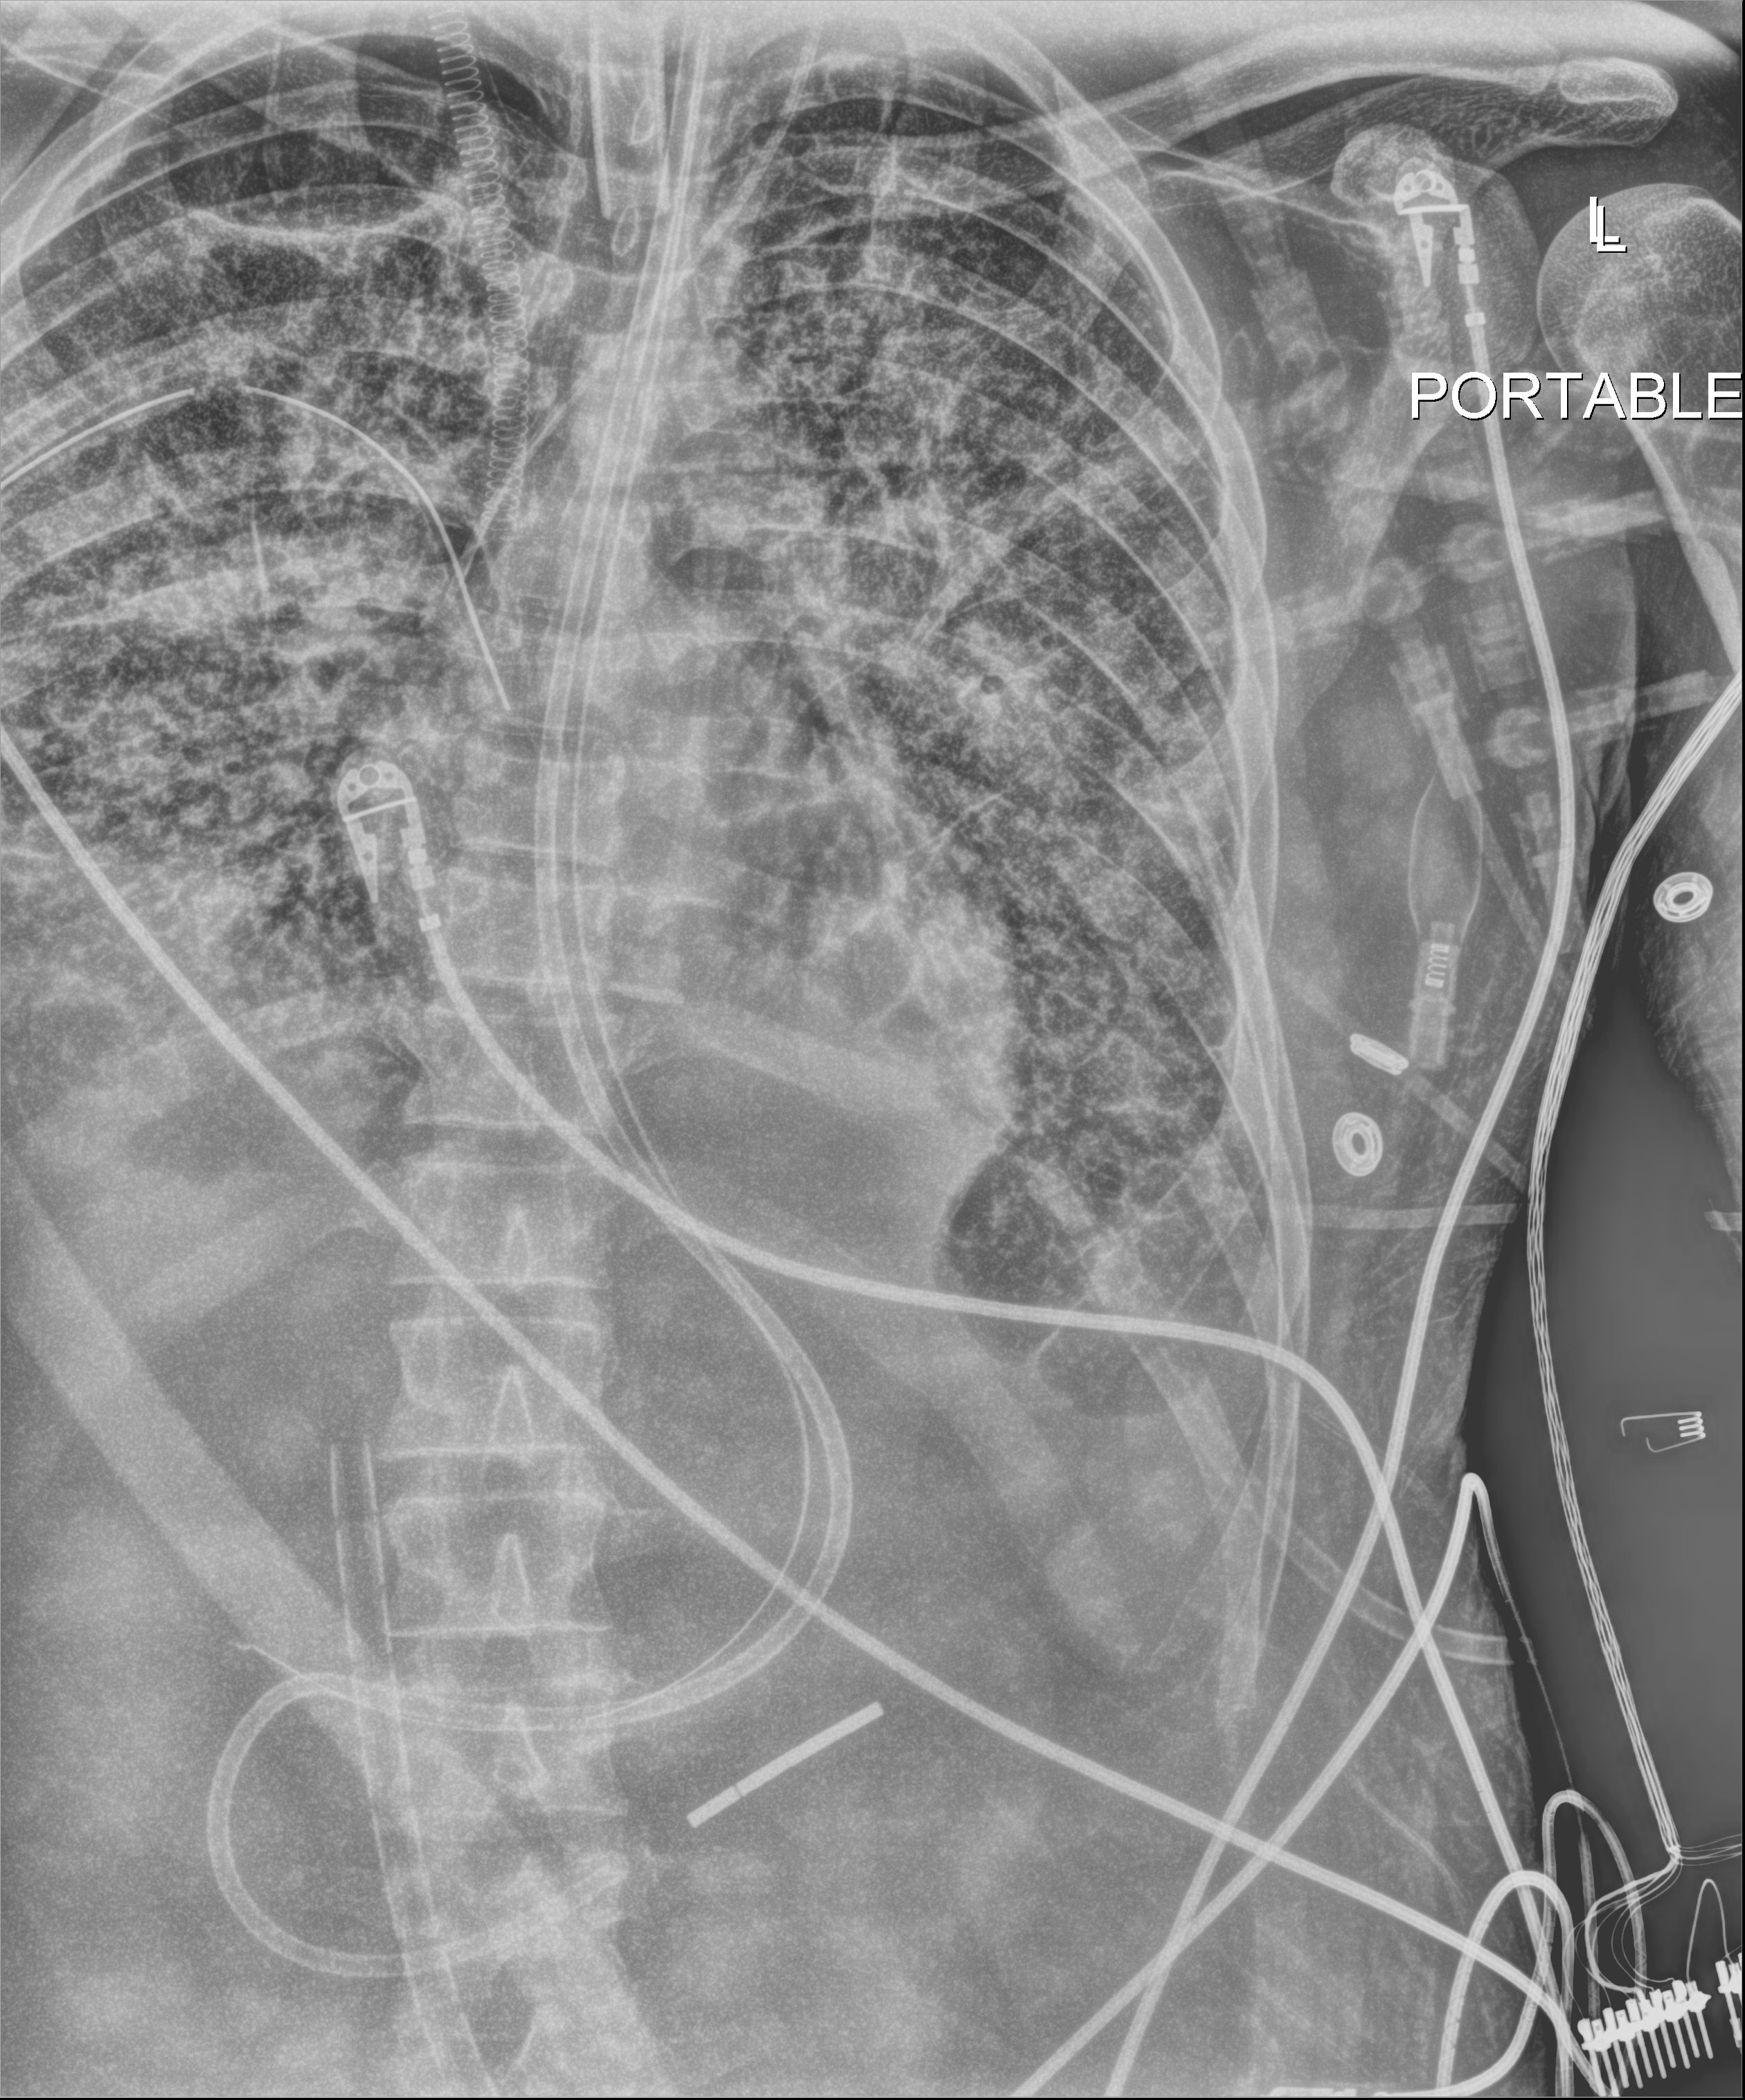
Bedside abdomen radiograph (digital radiography); anteroposterior (AP) projection. Adult patient hospitalised with COVID-19, age 18–59 years.
Hospital-stay facts (about this admission, not read from this image; timing relative to this image not recorded):
- mechanically ventilated during this hospital stay: yes
- admitted to intensive care during this hospital stay: yes
- smoking status (admission record): never